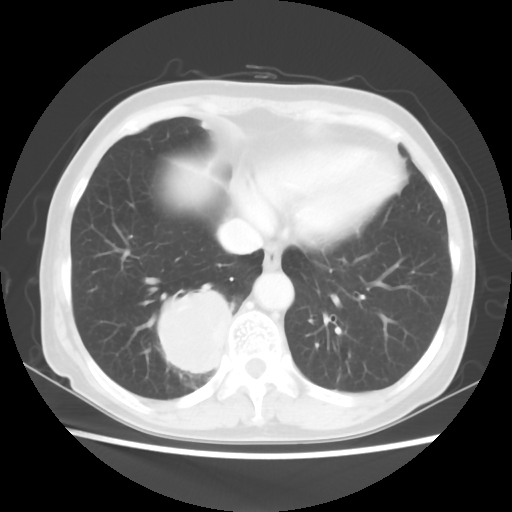
Chest CT, one axial slice; slice 16 of 56 in the series (ordered by position); reconstruction kernel STANDARD; 120 kVp; lung window (W 1500 / L -600 HU); 5 mm slice thickness; 512 × 512 image matrix, field of view 332 × 332 mm. Patient: female, 66 years. From the clinical record (not read from this slice): clinical TNM (as recorded): T2 N3 M0; histopathological grade: G3.
Annotated regions visible in this slice (rectangle marked by the reading radiologist):
- lung tumour (recorded histology: small cell carcinoma): bounding box [x1, y1, x2, y2] px = [159, 282, 240, 394]